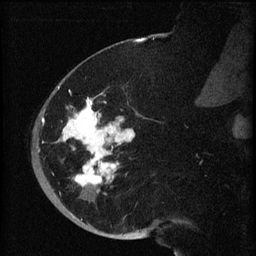
Breast MRI (dynamic contrast-enhanced), one sagittal slice; position 22 of 60 along the scan axis; dynamic contrast-enhanced series, image 2 of 3 at this slice position (ordered by acquisition); 1.5 T; TE 4.2 ms, TR 8.2 ms; 256 × 256 image matrix, field of view 180 × 180 mm. Female patient, age 71 years.
Outlined on this slice (semi-automatically segmented with operator editing):
- analysis volume of interest (the breast-tissue region the enhancement analysis was run in; not a lesion): box from (x=40, y=72) to (x=148, y=196) px
- tumour enhancement mask (voxels above the 70 % enhancement threshold inside the analysis volume of interest): (x=41, y=86)–(x=135, y=192)